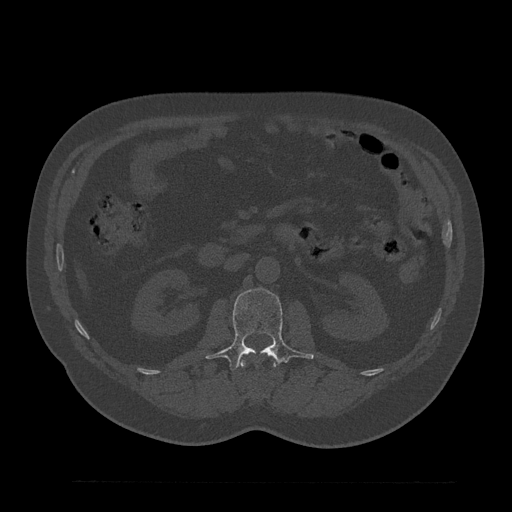
CT including the spine, one axial slice. Slice 111 of 797 in the series (ordered by position). 120 kVp. Bone window (W 1800 / L 400 HU). 0.5 mm slice thickness. 512 × 512 image matrix, field of view 430 × 430 mm. Male patient, age 61 years. Case-level facts recorded for this patient, not image findings: primary cancer: prostate.
Structures marked on this image (semi-automatically segmented with operator editing):
- L1 vertebra: bounding box (x1, y1, x2, y2) in pixels: (241, 351, 277, 400)
- L2 vertebra: (207, 288, 314, 371)